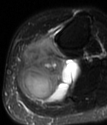
MRI of an extremity soft-tissue mass, one axial slice. Slice 36 of 78 in the series (ordered by position). T2-weighted fat-saturated. MR volume resampled by the dataset authors to the PET/CT grid (not the native acquisition matrix). 3.27 mm slice thickness. 107 × 125 image matrix, field of view 104 × 122 mm. Female patient. Case-level facts recorded for this patient, not image findings: histological type: extraskeletal high grade osteogenic sarcoma; grade: high; site of the primary tumour: left calf.
Structures marked on this image (expert contour drawn on MRI and transferred to this co-registered scan by the dataset authors):
- gross tumour volume (mass): bounding box [x1, y1, x2, y2] px = [17, 38, 79, 103]